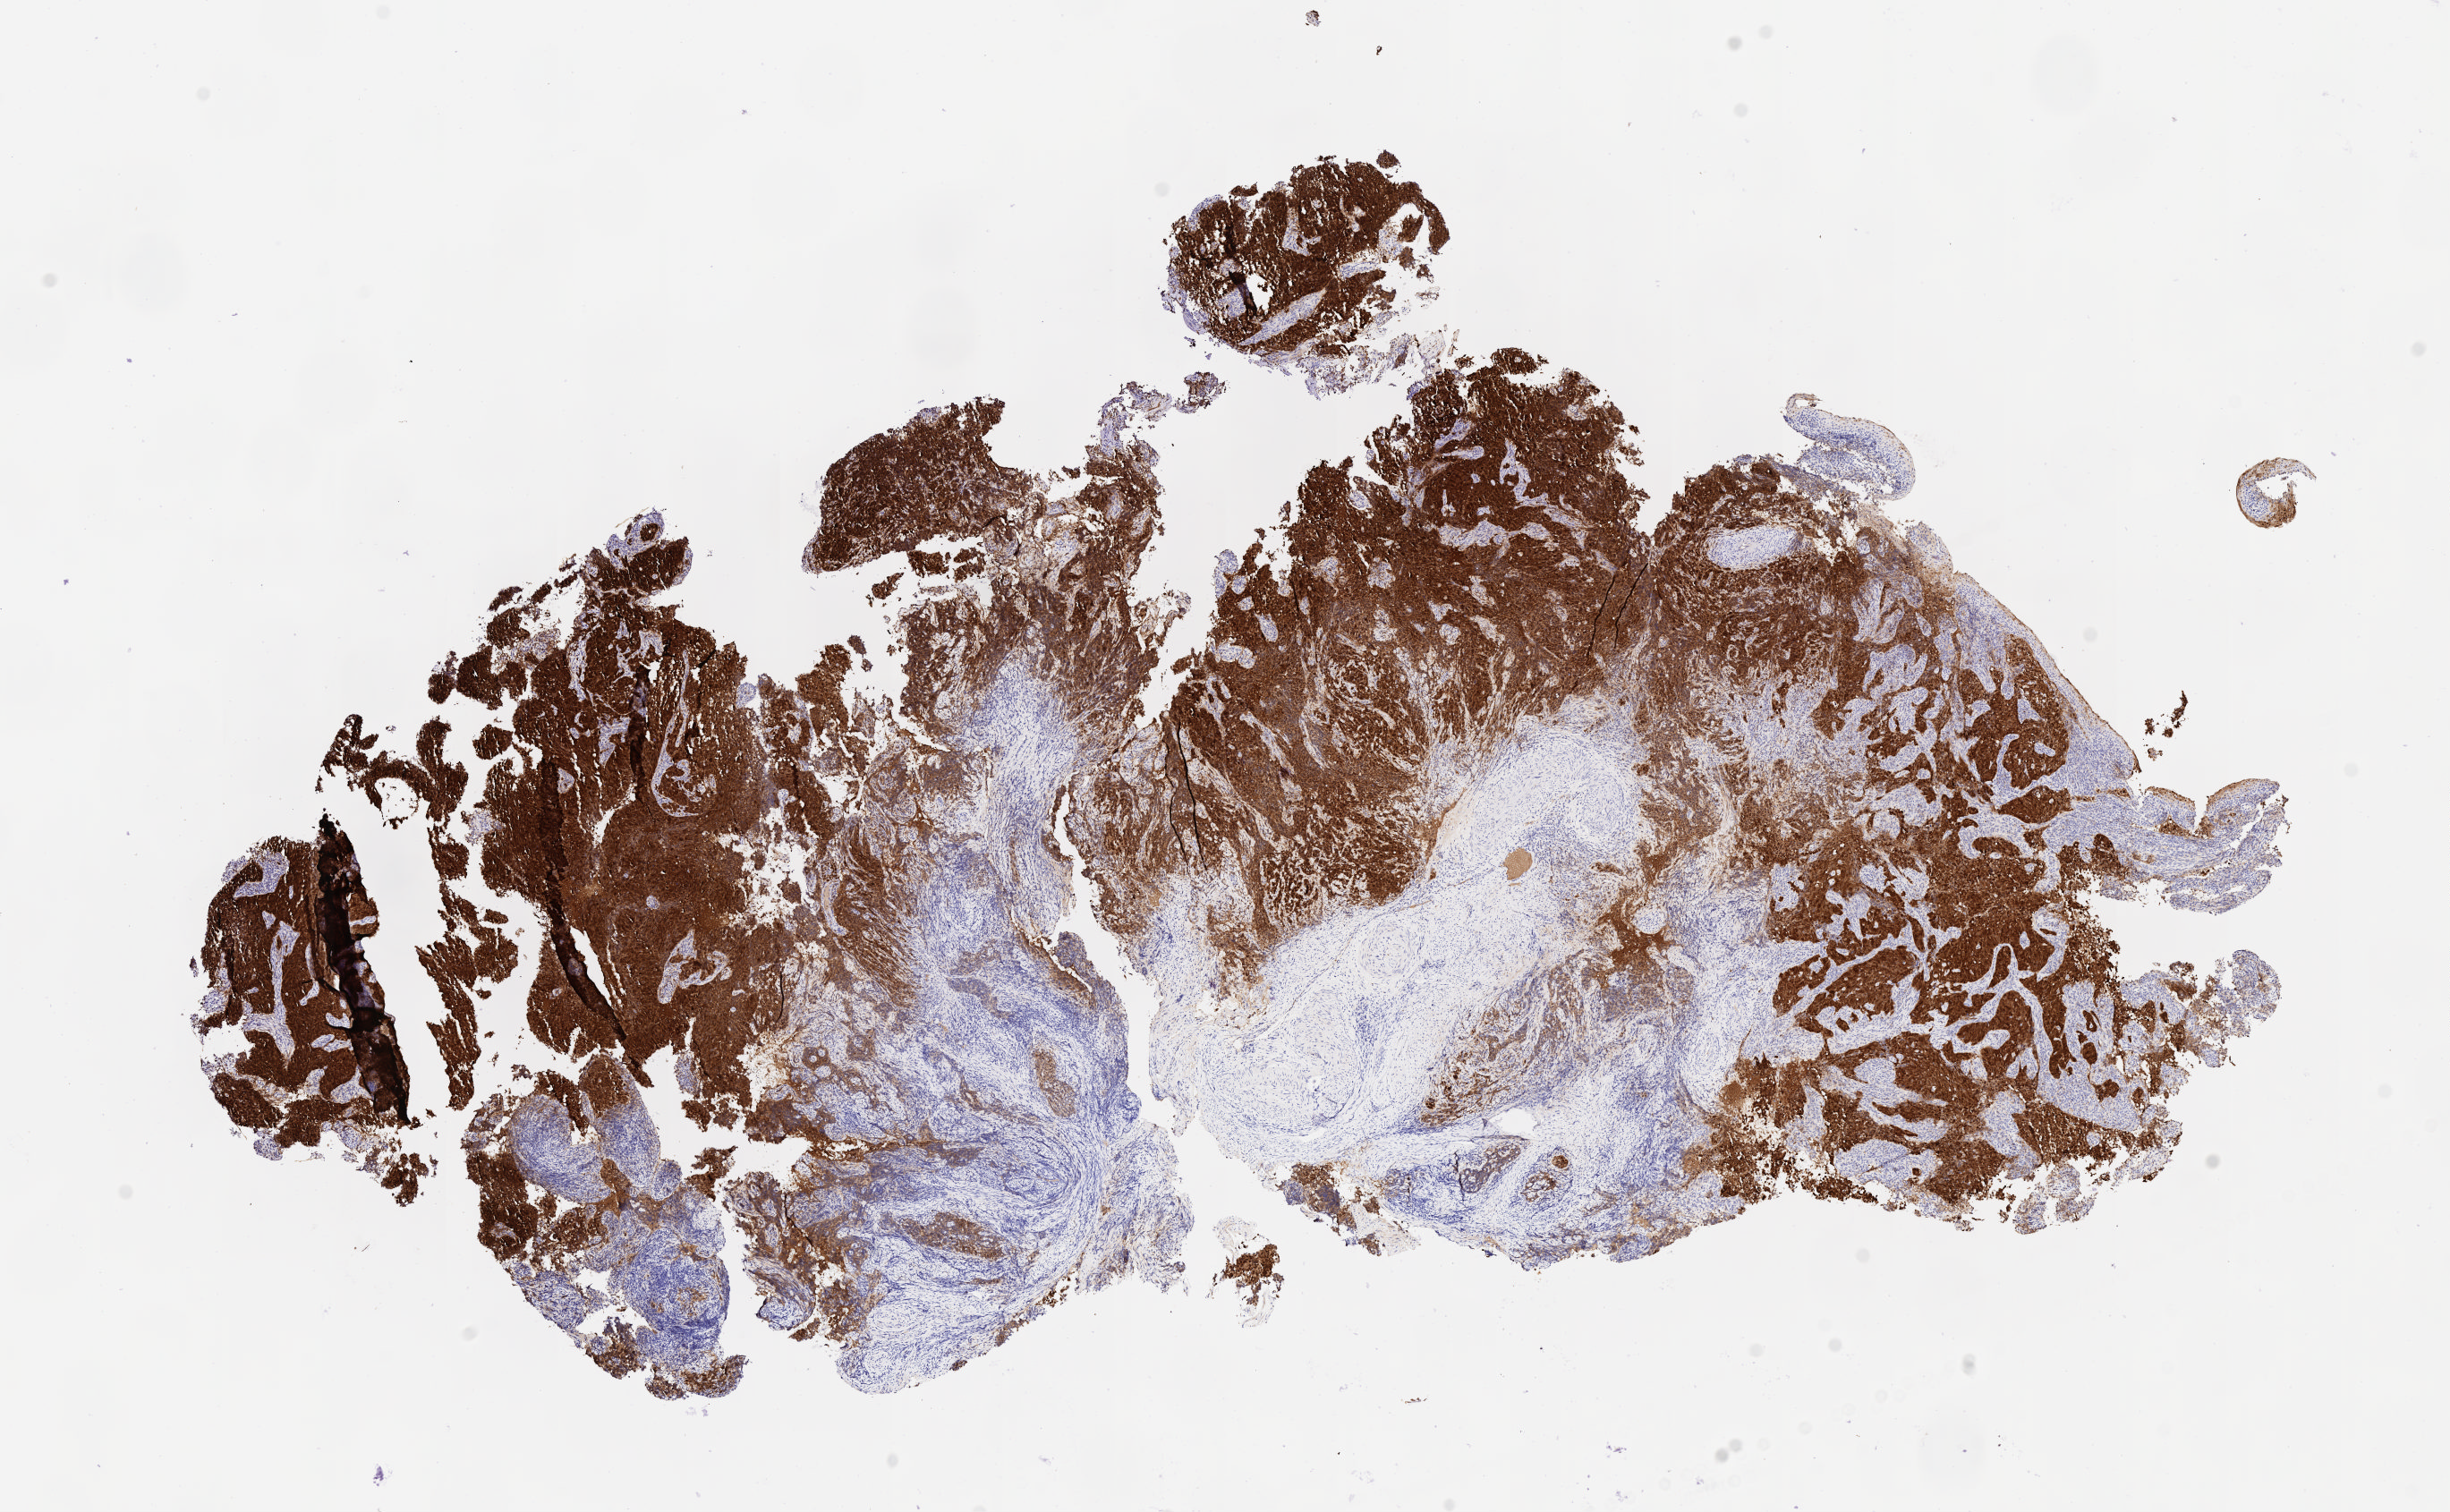
IHC for p16 (p16INK4a), whole-slide image — shown as a low-resolution overview of the whole scanned area (about 11.1 x 6.8 mm). Specimen: tumor tissue. Site: cervix. Patient: female, aged 48.
• diagnosis: Squamous cell carcinoma, large cell, nonkeratinizing, NOS